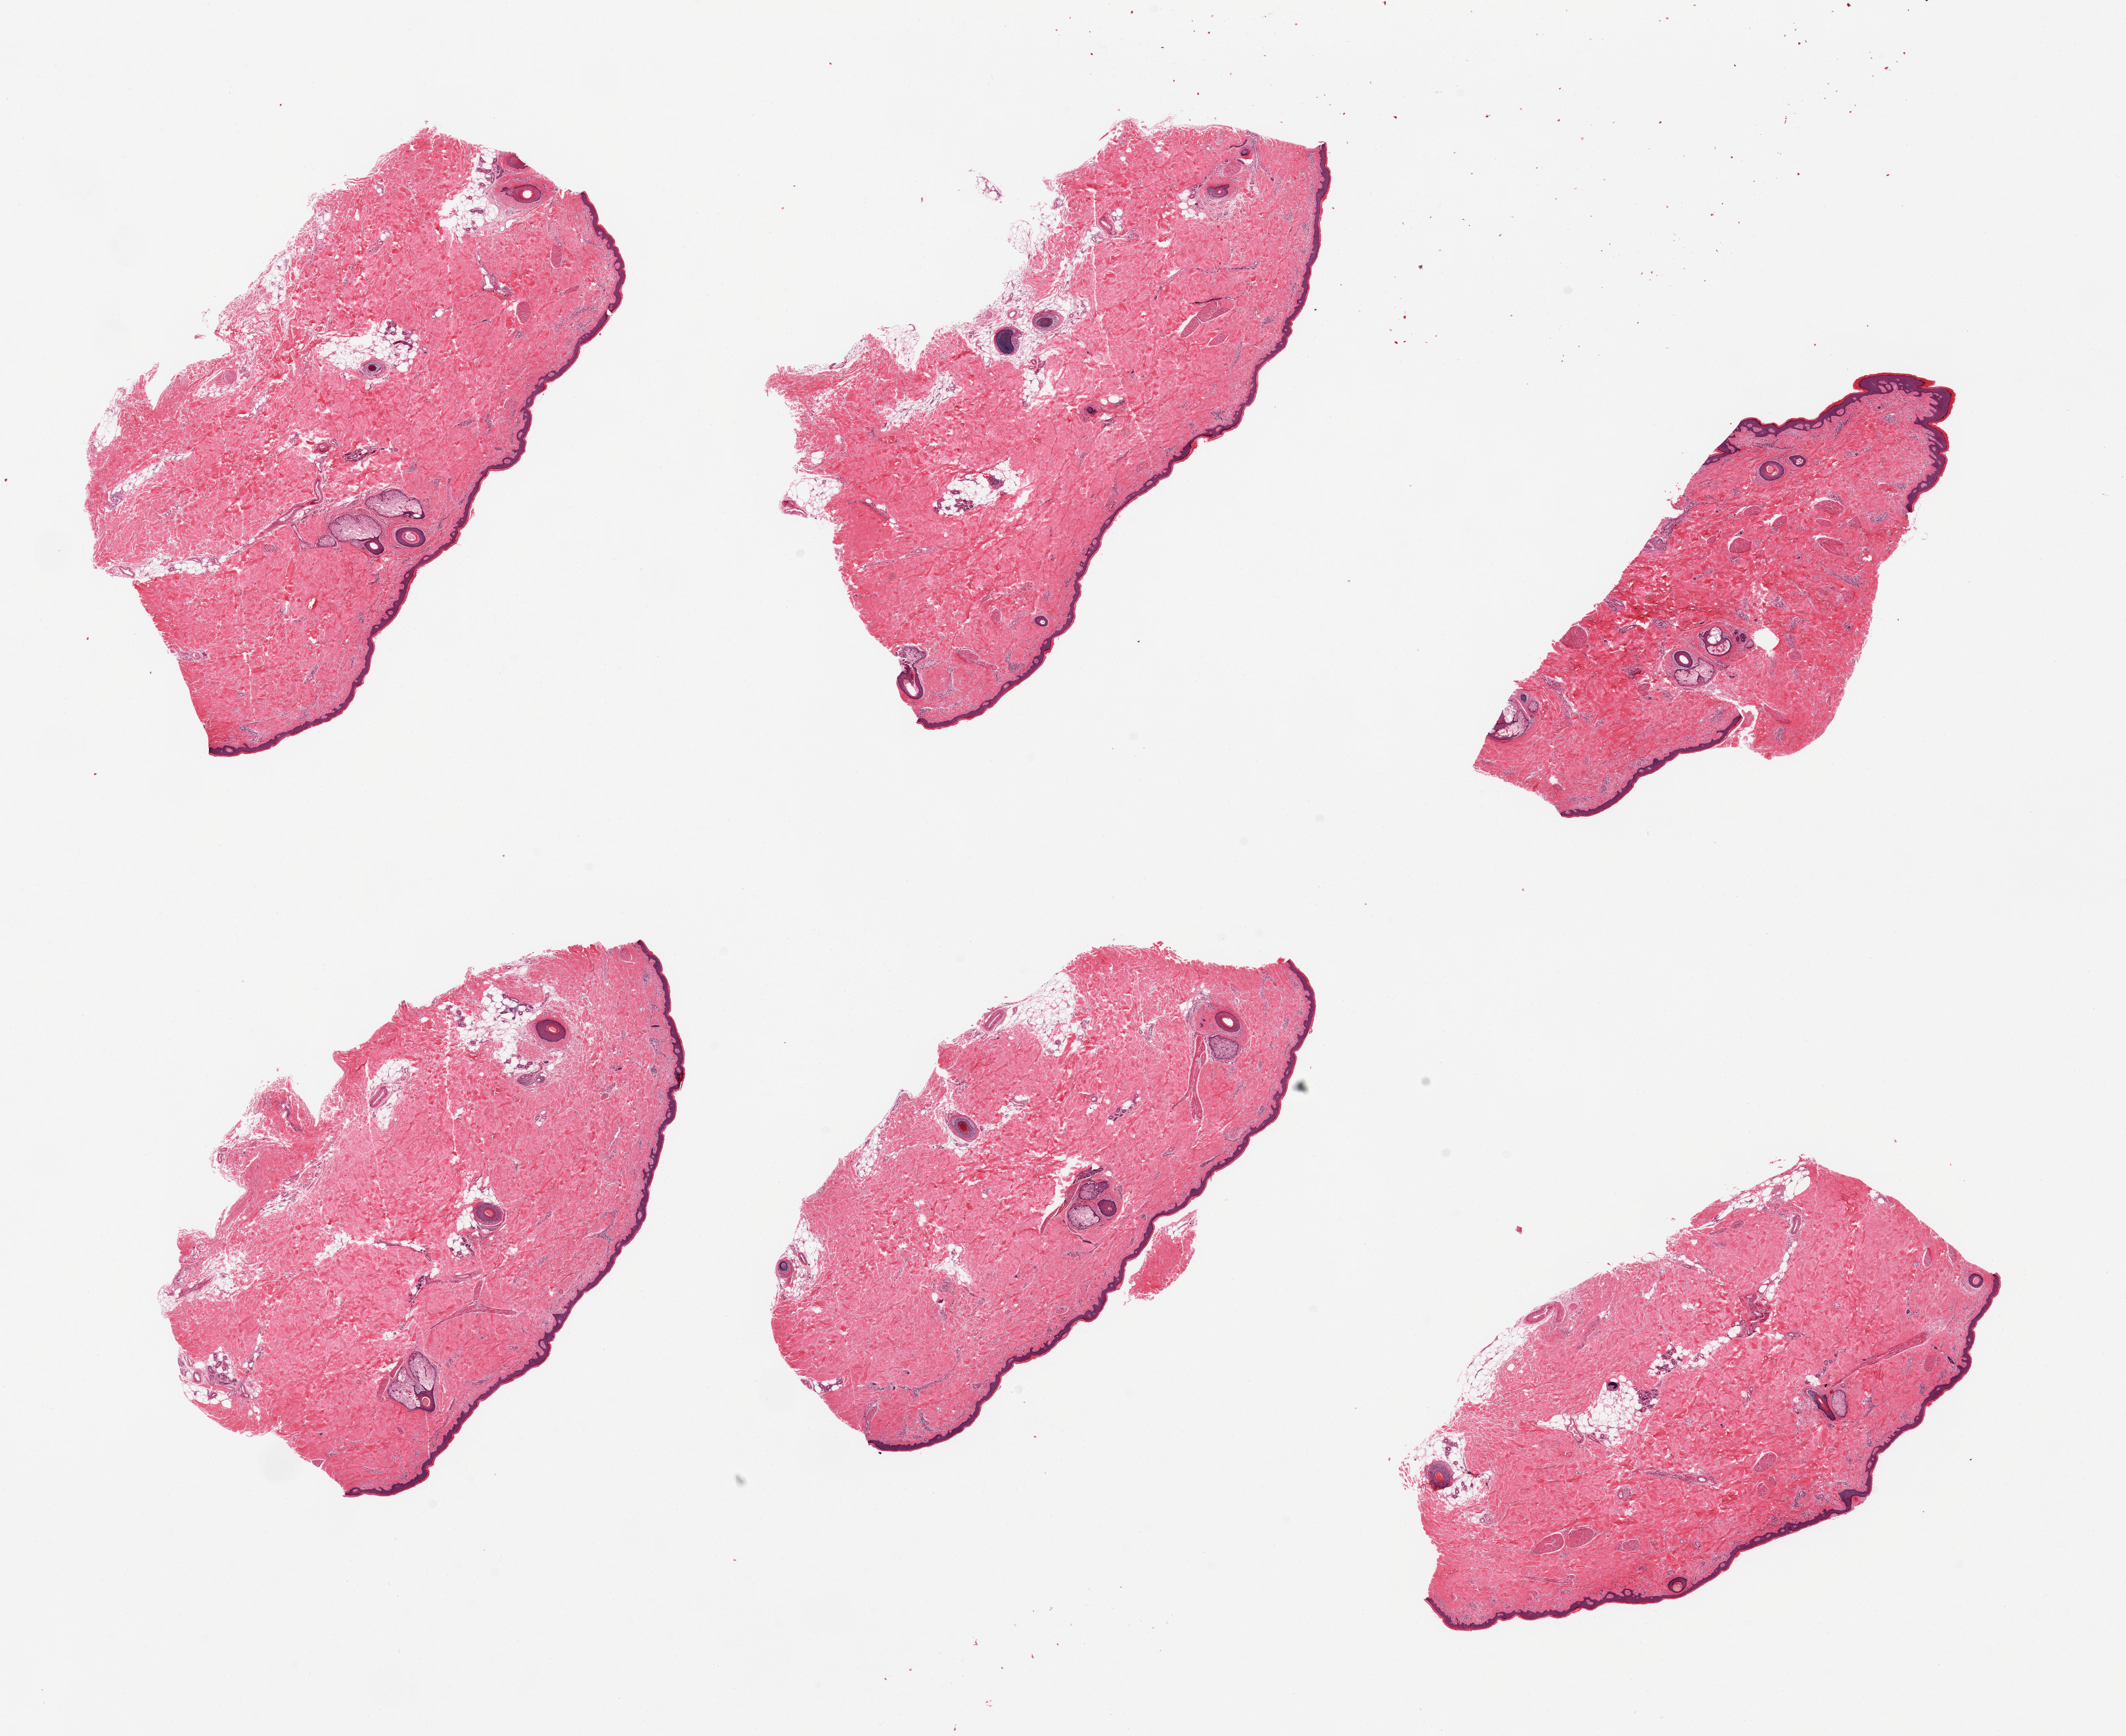
Hematoxylin and eosin (H&E) whole-slide image — low-resolution overview of the scanned area, about 25.6 x 20.9 mm. PAXgene-fixed paraffin-embedded (PFPE) section. Sampled site (target tissue): skin of lower leg. Donor tissue sample. Donor: male.
• pathologist's review note for this sample: 6 pieces; well; trimmed; contains 10% internal fat